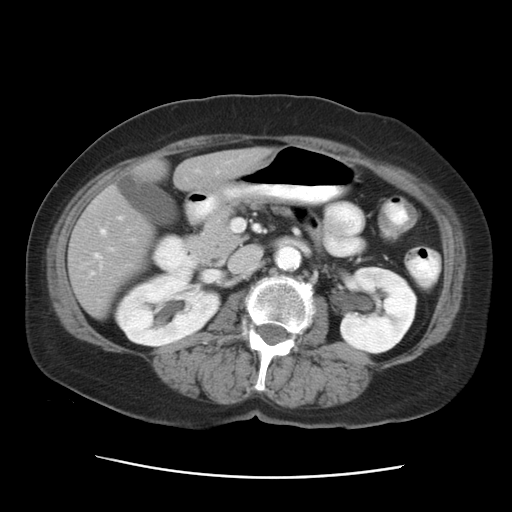
Contrast-enhanced abdominal CT, one axial slice. Slice 12 of 29 in the series (ordered by position). 120 kVp. Intravenous contrast given. Soft-tissue window (W 400 / L 40 HU). 7.5 mm slice thickness. 512 × 512 image matrix. Female patient, age 64 years. From the clinical record (not read from this slice): diagnosis: colorectal cancer liver metastases, imaged before liver resection; multiple liver metastases: no.
Annotated regions visible in this slice (expert manual segmentation):
- hepatic veins: bounding box <95,229,106,258> (left, top, right, bottom; pixels)
- liver: <68,148,271,316>
- planned liver remnant (the part of the liver to remain after resection): <68,148,270,316>
- portal vein (with intrahepatic branches): <119,217,237,232>